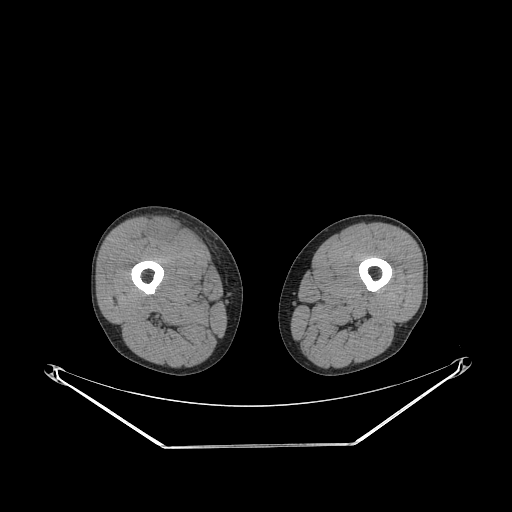
CT of an extremity soft-tissue mass (from a PET/CT study), one axial slice. Slice 242 of 311 in the series (ordered by position). Reconstruction kernel STANDARD. 140 kVp. Soft-tissue window (W 400 / L 40 HU). 3.75 mm slice thickness. 512 × 512 image matrix, field of view 500 × 500 mm. Male patient. From the clinical record (not read from this slice): histological type: pleiomorphic leiomyosarcoma; grade: intermediate; site of the primary tumour: right thigh.
Outlined on this slice (expert contour drawn on MRI and transferred to this co-registered scan by the dataset authors):
- gross tumour volume including surrounding oedema: bounding box (x1, y1, x2, y2) in pixels: (149, 219, 182, 243)